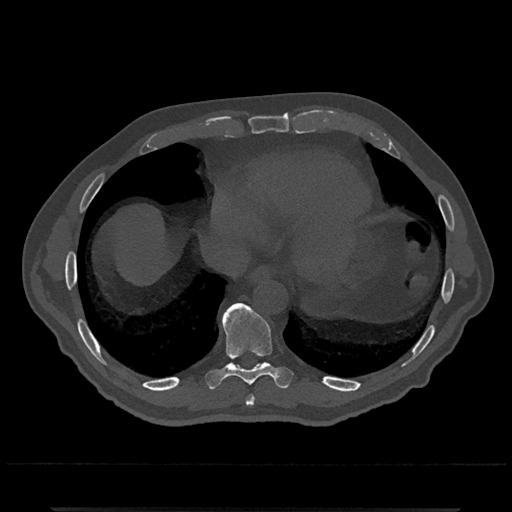
CT including the spine, one axial slice; bone window (W 1800 / L 400 HU); 0.5 mm slice thickness; 512 × 512 image matrix, field of view 393 × 393 mm. Patient: male, 67 years. From the clinical record (not read from this slice): primary cancer: prostate.
Outlined on this slice (semi-automatic segmentation, software-assisted and operator-edited):
- T8 vertebra: bounding box [x1, y1, x2, y2] px = [246, 395, 255, 406]
- T9 vertebra: [205, 303, 293, 389]